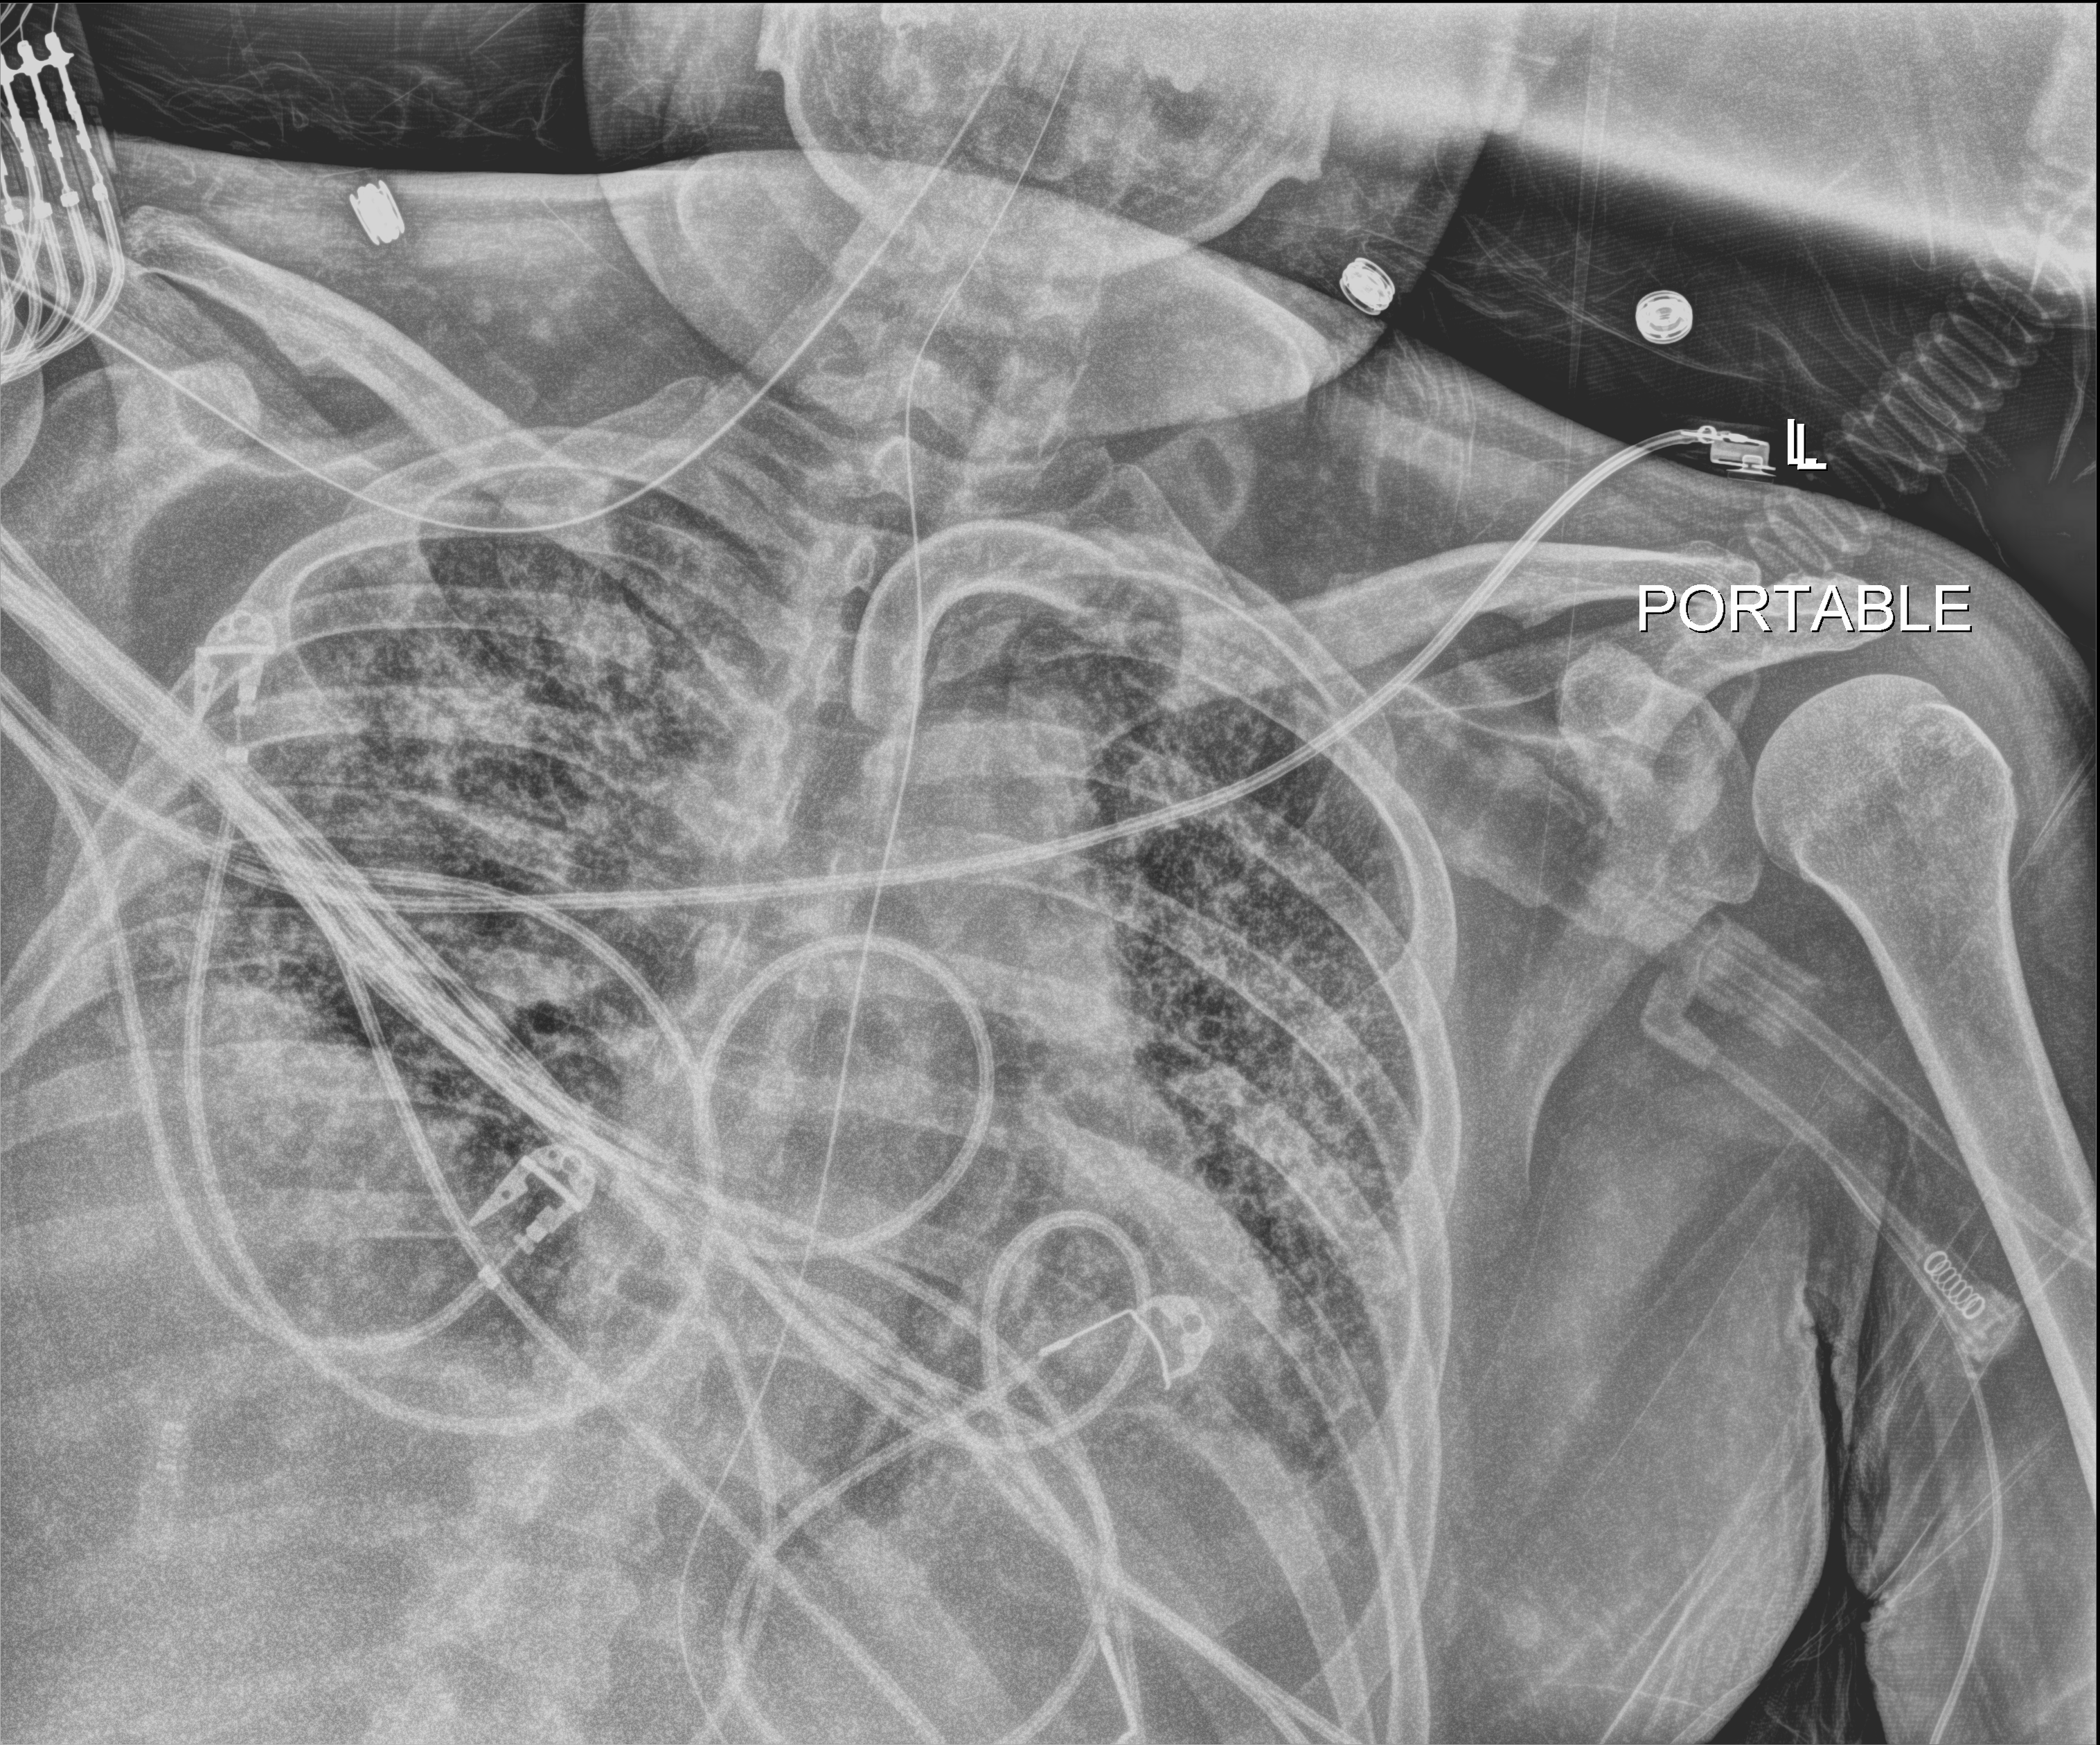
Portable chest radiograph, anteroposterior (AP) projection. Patient hospitalised with COVID-19; male, aged 18–59 years.
From the hospital-stay record, not from the radiograph (when in the stay this image was taken is not recorded):
- admitted to intensive care during this hospital stay: yes
- hypertension (admission record): no